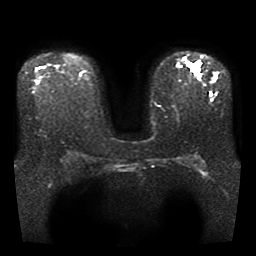
Breast MRI, one axial slice; diffusion-weighted series; image 2 of 4 stored at this slice position (different b-values; order by instance number); 1.5 T; 256 × 256 image matrix, field of view 330 × 330 mm. Female patient.
Structures marked on this image (outlined manually by an expert reader):
- tumour on diffusion-weighted imaging: box from (x=187, y=62) to (x=199, y=76) px